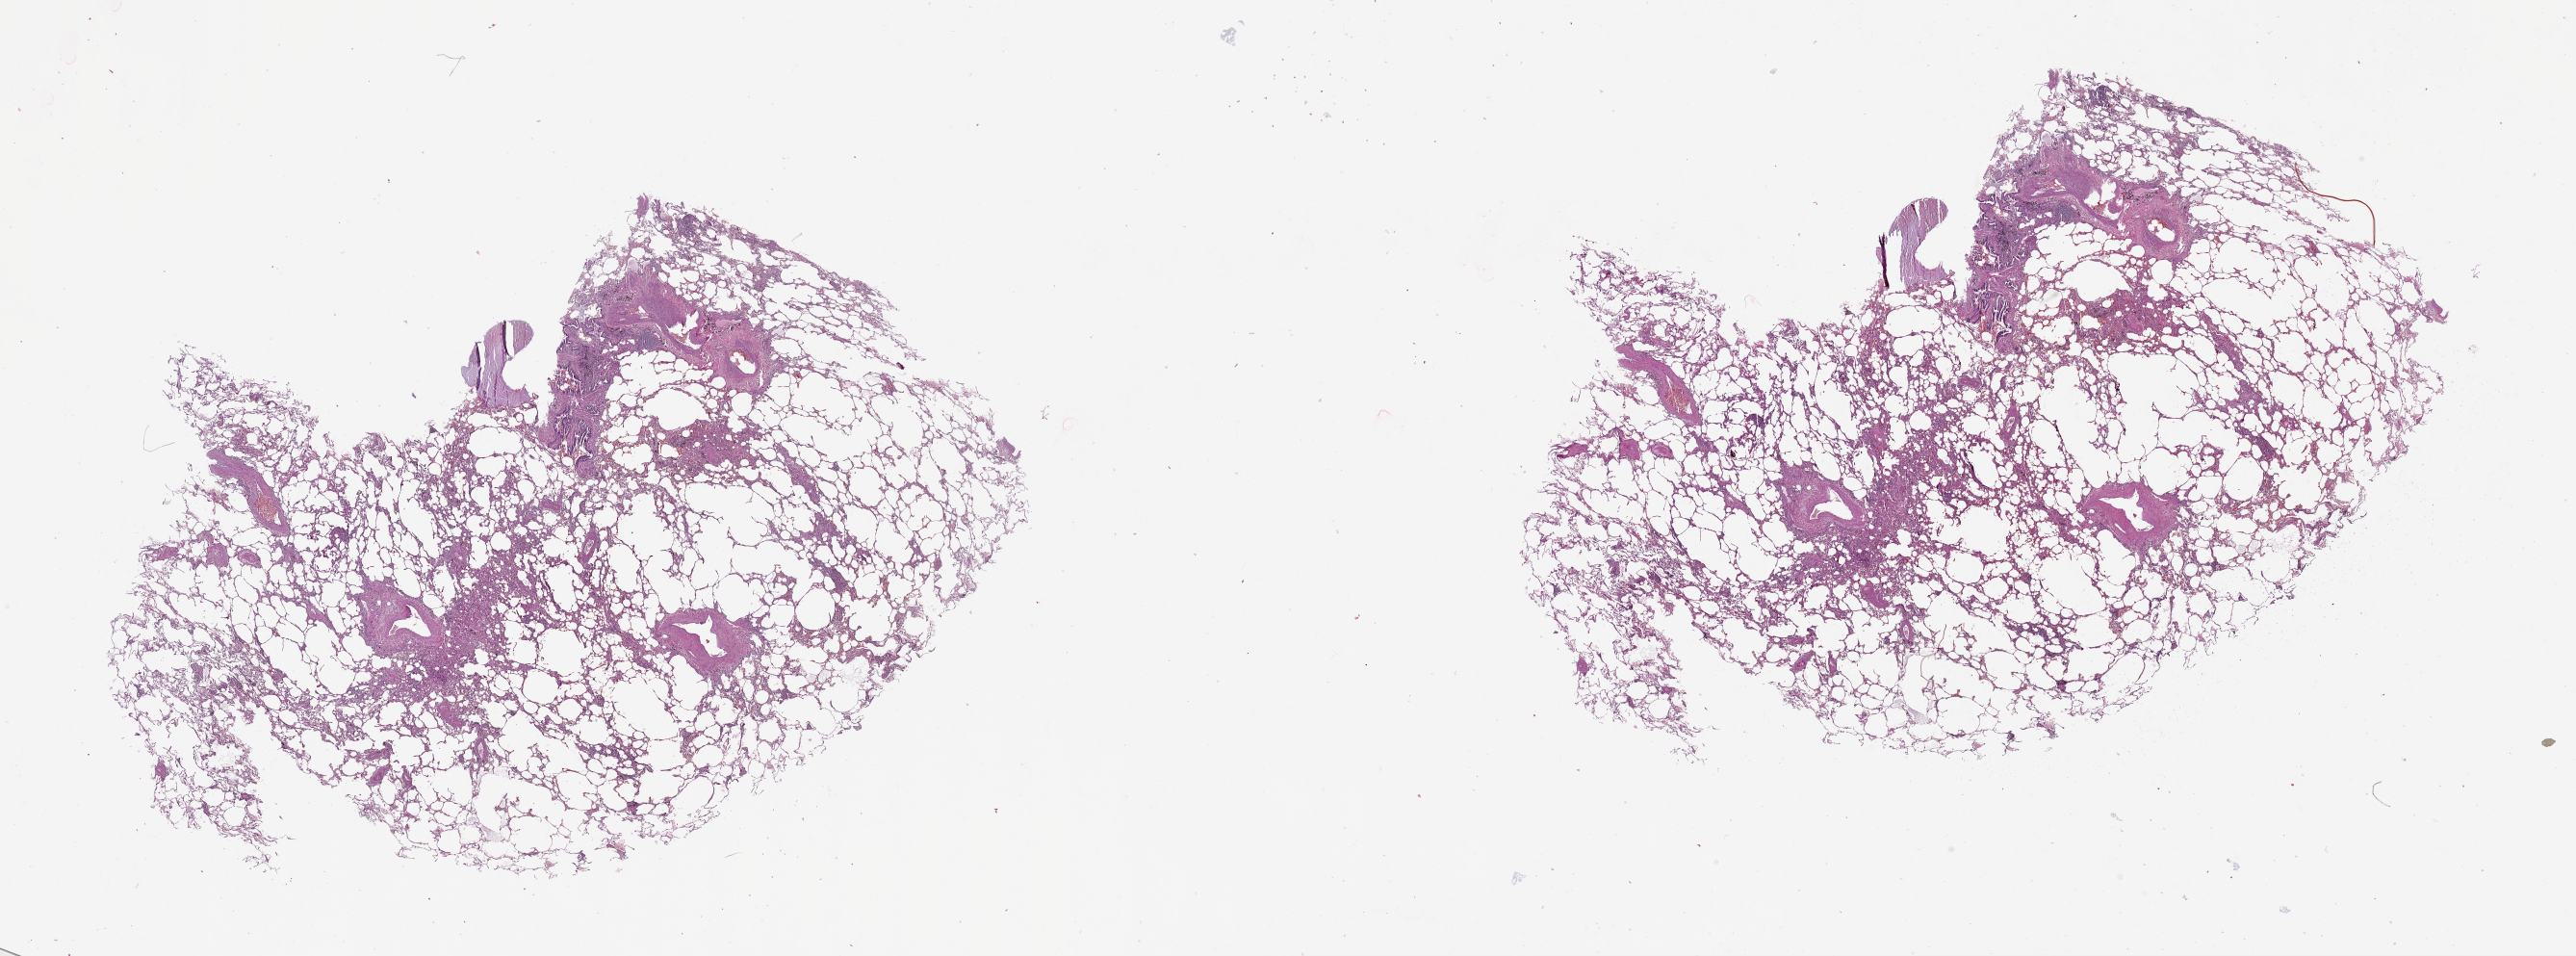
Whole-slide histology image, H&E, a low-resolution overview of the entire scanned area, about 43.1 x 16.0 mm (slide scanned at 20x), normal (non-tumour) tissue sample, lung. Patient: male, age 58 years.
- this section: normal (non-tumour) tissue from the same patient
- patient diagnosis (cohort enrolment): squamous cell carcinoma (lung)